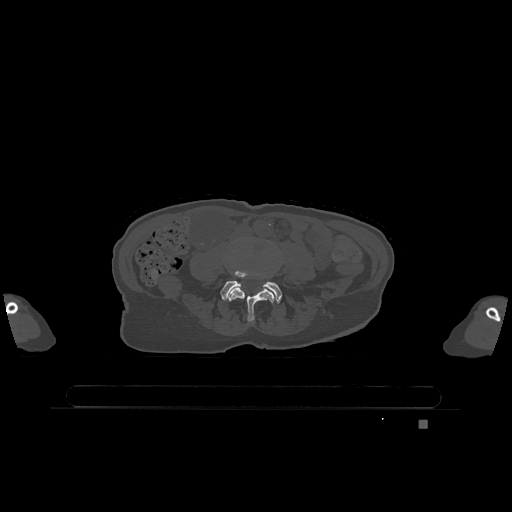
CT including the spine, one axial slice; position 270 of 1317 along the scan axis; bone window (W 1800 / L 400 HU); 512 × 512 image matrix, field of view 500 × 500 mm. Female patient, age 74 years. Case-level facts recorded for this patient, not image findings: primary cancer: lung.
Structures marked on this image (semi-automatic segmentation, software-assisted and operator-edited):
- L4 vertebra: bounding box (x1, y1, x2, y2) in pixels: (228, 288, 274, 322)
- L5 vertebra: (220, 272, 282, 303)